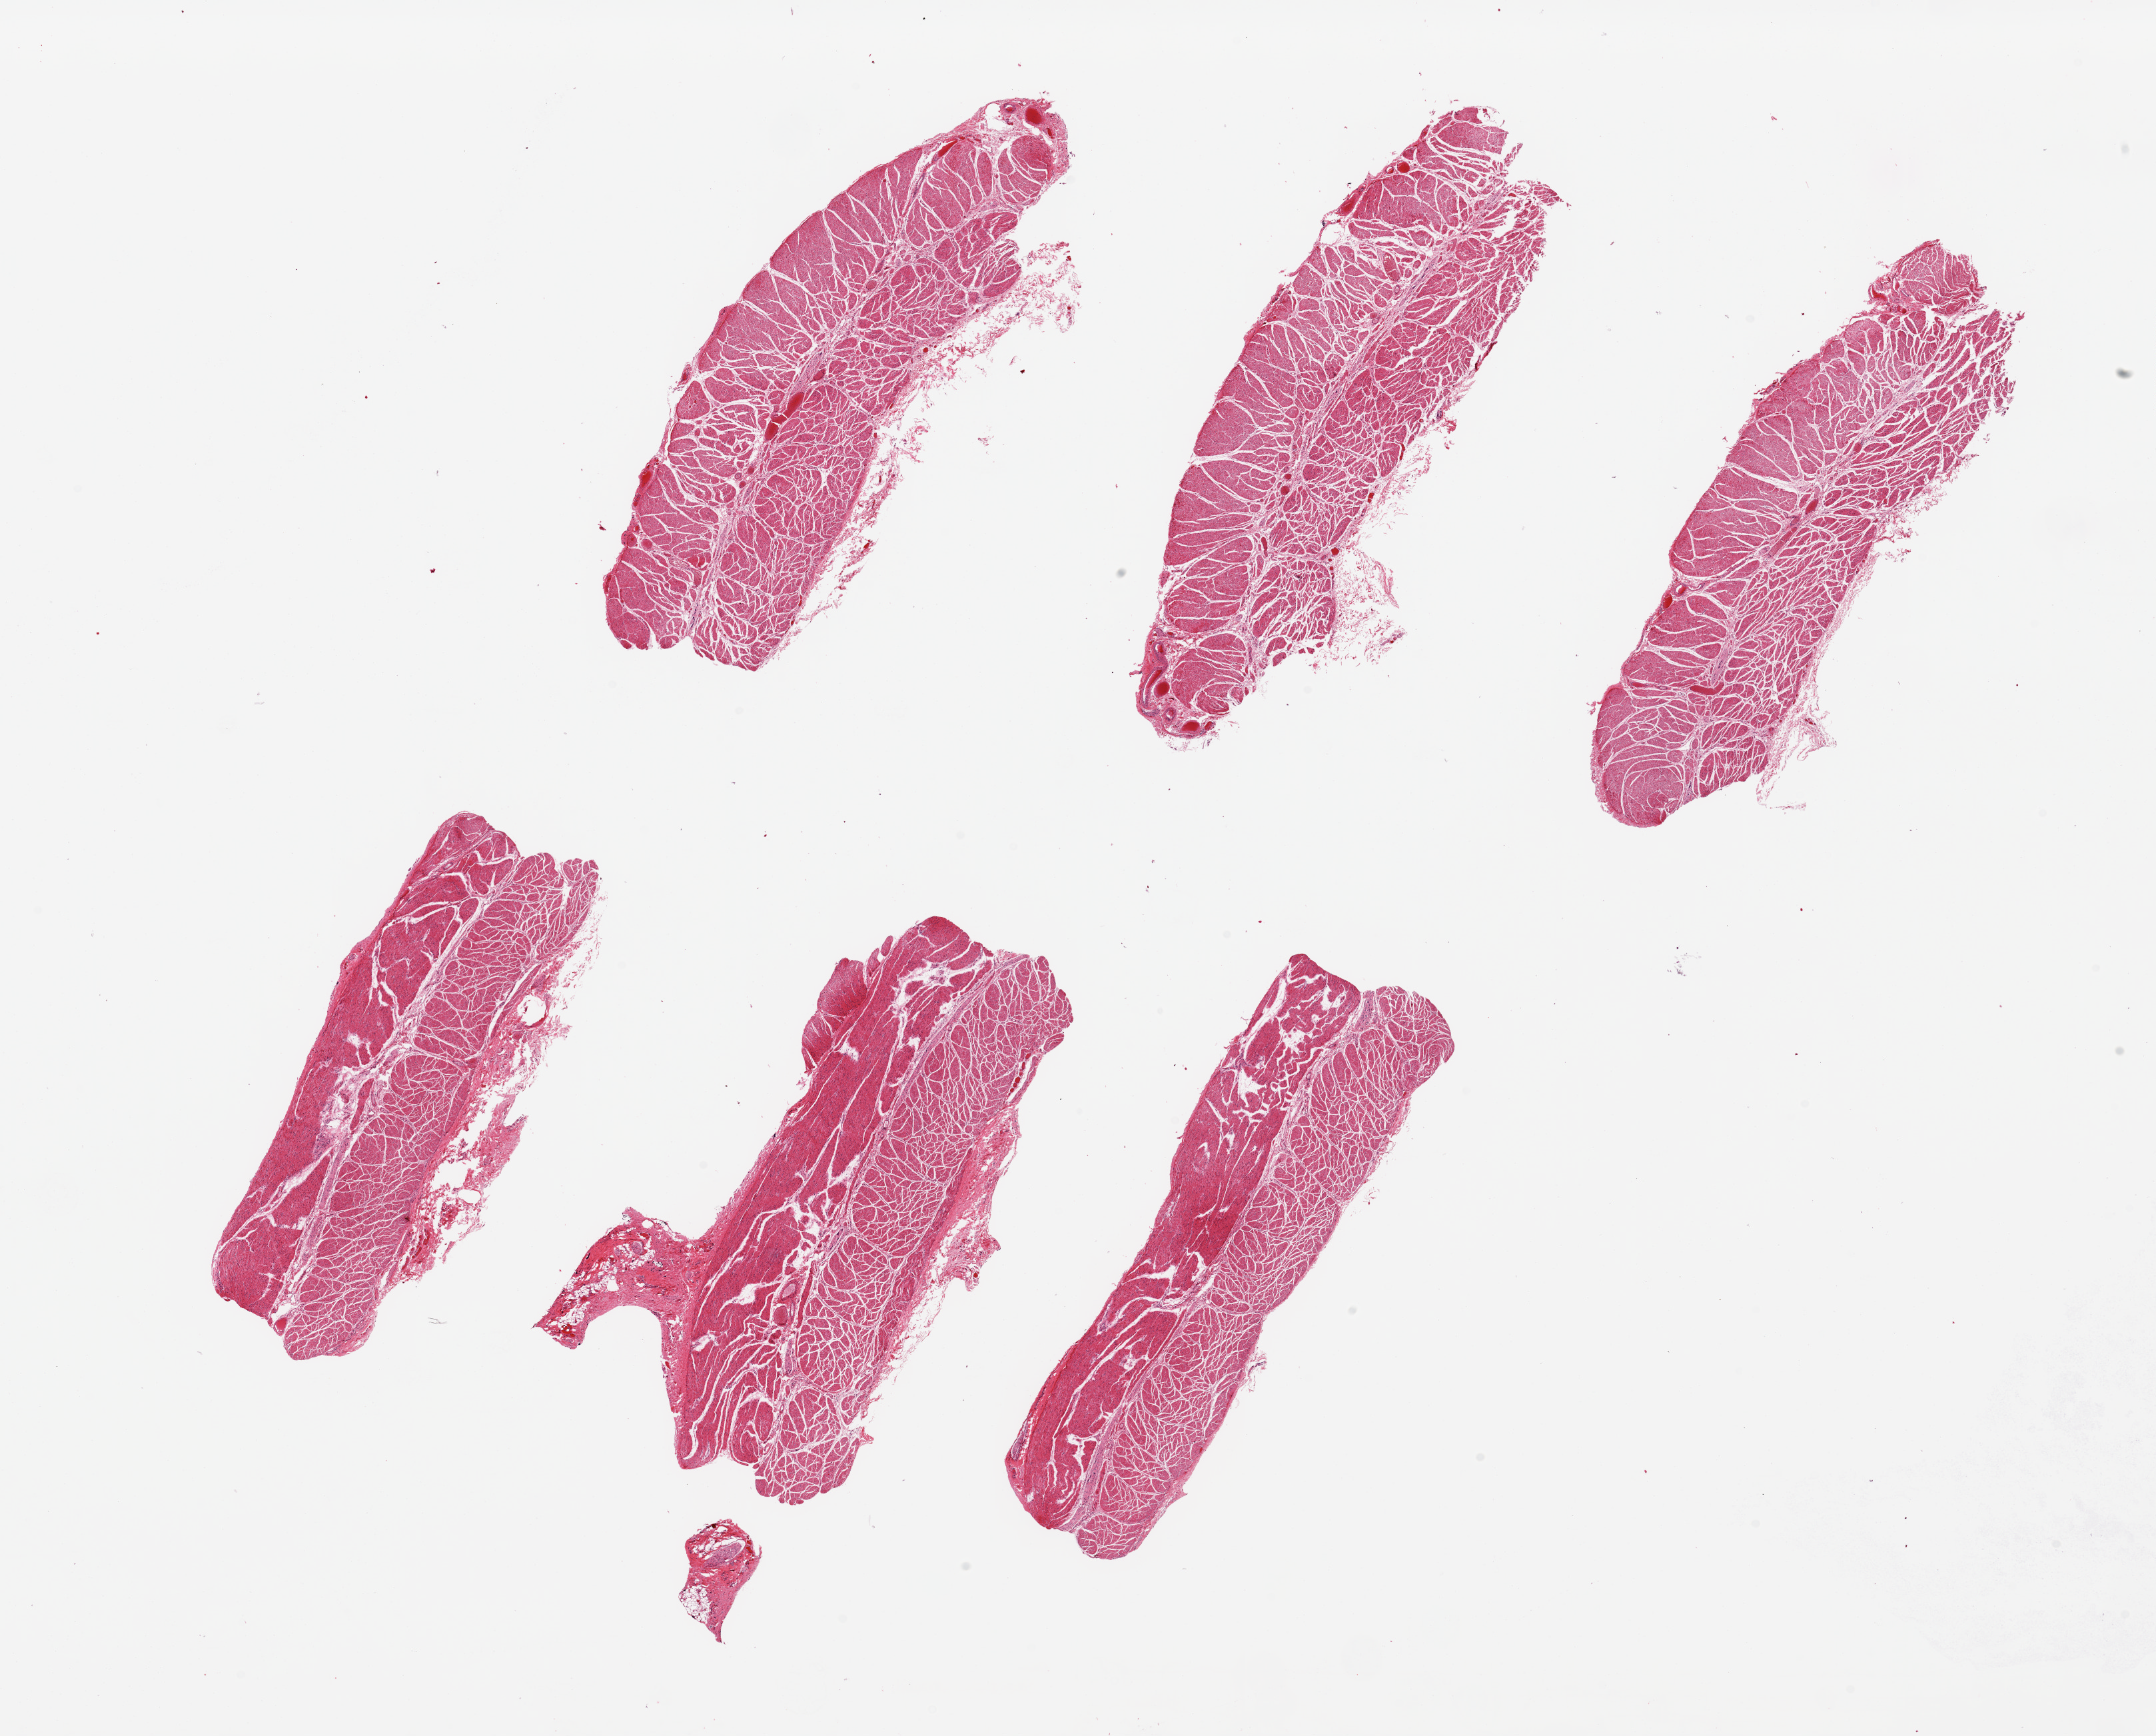
Hematoxylin and eosin (H&E) whole-slide image — shown as a low-resolution overview of the whole scanned area (about 25.6 x 20.6 mm); PAXgene-fixed, paraffin-embedded tissue; sampled site (target tissue): esophageal muscle; tissue donor sample.
• reviewer comment on this tissue sample: 6 pieces up to 7x3 mm; all are muscularis propria; re-label as Esophagus - muscularis